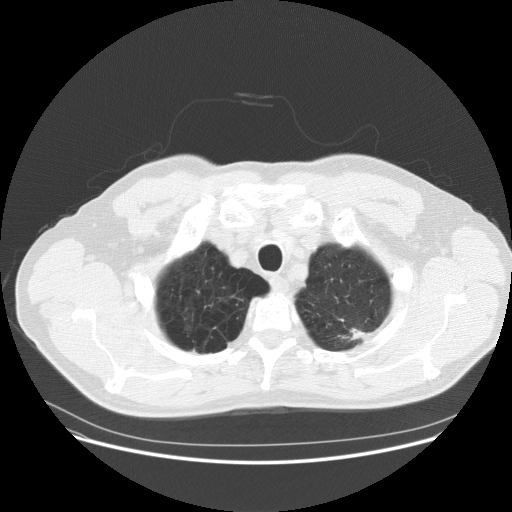
Low-dose screening chest CT, axial slice, baseline screening round, lung window (W 1500 / L -600 HU), 2.5 mm slice thickness, 120 kVp, slice 13 of 158 in the series. Male, age 61 years at enrolment. Current smoker at enrolment.
Lesion marked by an expert reader, box from (x=325, y=308) to (x=390, y=361) px. Reader record for this screening exam (exam-level; its link to the box is not recorded): non-calcified nodule or mass ≥4 mm, left upper lobe, 12 × 6 mm, poorly defined margins, soft tissue attenuation. Later outcome: lung cancer diagnosed 317 days after this screen — adenocarcinoma, NOS, left upper lobe, poorly differentiated (G3), stage IIIA (AJCC 6th edition), 30 mm at pathology.